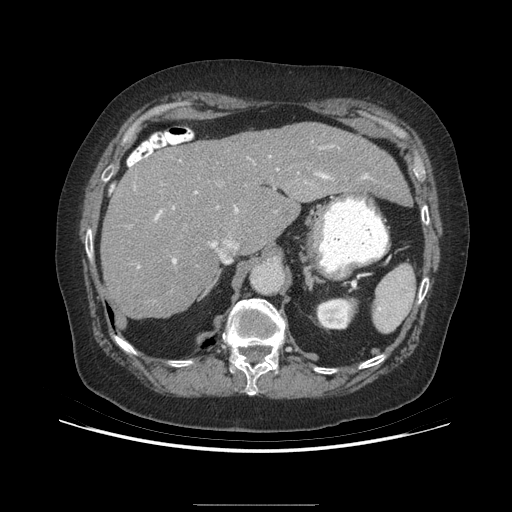
Contrast-enhanced abdominal CT (liver protocol), one axial slice; slice 163 of 192 in the series (ordered by position); reconstruction kernel STANDARD; 140 kVp; soft-tissue window (W 400 / L 40 HU); 2.5 mm slice thickness; 512 × 512 image matrix, field of view 400 × 400 mm. From the clinical record (not read from this slice): diagnosis: hepatocellular carcinoma (patient treated with transarterial chemoembolisation; whether this scan precedes or follows treatment is not stated here); TNM stage (as recorded): Stage-I; Child-Pugh class: A; tumour differentiation: moderately differentiated; tumour size: 3.2 cm.
Outlined on this slice (semi-automatic segmentation, software-assisted and operator-edited):
- liver parenchyma outside the tumour (the mass and vessels are separate outlines, so this box may not span the whole liver): bounding box [x1, y1, x2, y2] px = [100, 124, 408, 318]
- liver vessels: [137, 173, 368, 268]